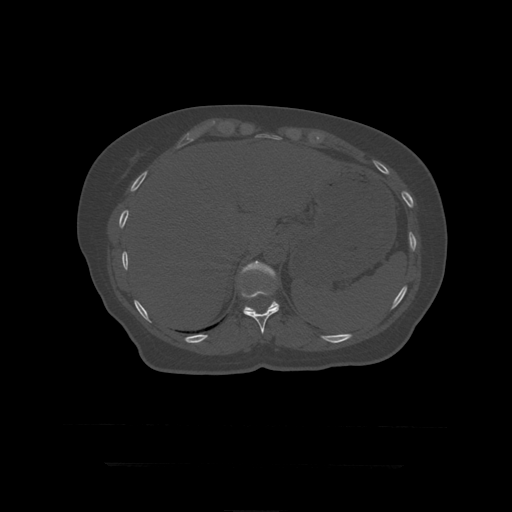
CT including the spine, one axial slice. Slice 213 of 399 in the series (ordered by position). Reconstruction kernel STANDARD. 120 kVp. Bone window (W 1800 / L 400 HU). 1.25 mm slice thickness. 512 × 512 image matrix. Patient age 41 years. From the clinical record (not read from this slice): primary cancer: breast.
Outlined on this slice (semi-automatic segmentation, software-assisted and operator-edited):
- T11 vertebra: bounding box (x1, y1, x2, y2) in pixels: (242, 286, 280, 334)
- T12 vertebra: (240, 261, 279, 312)